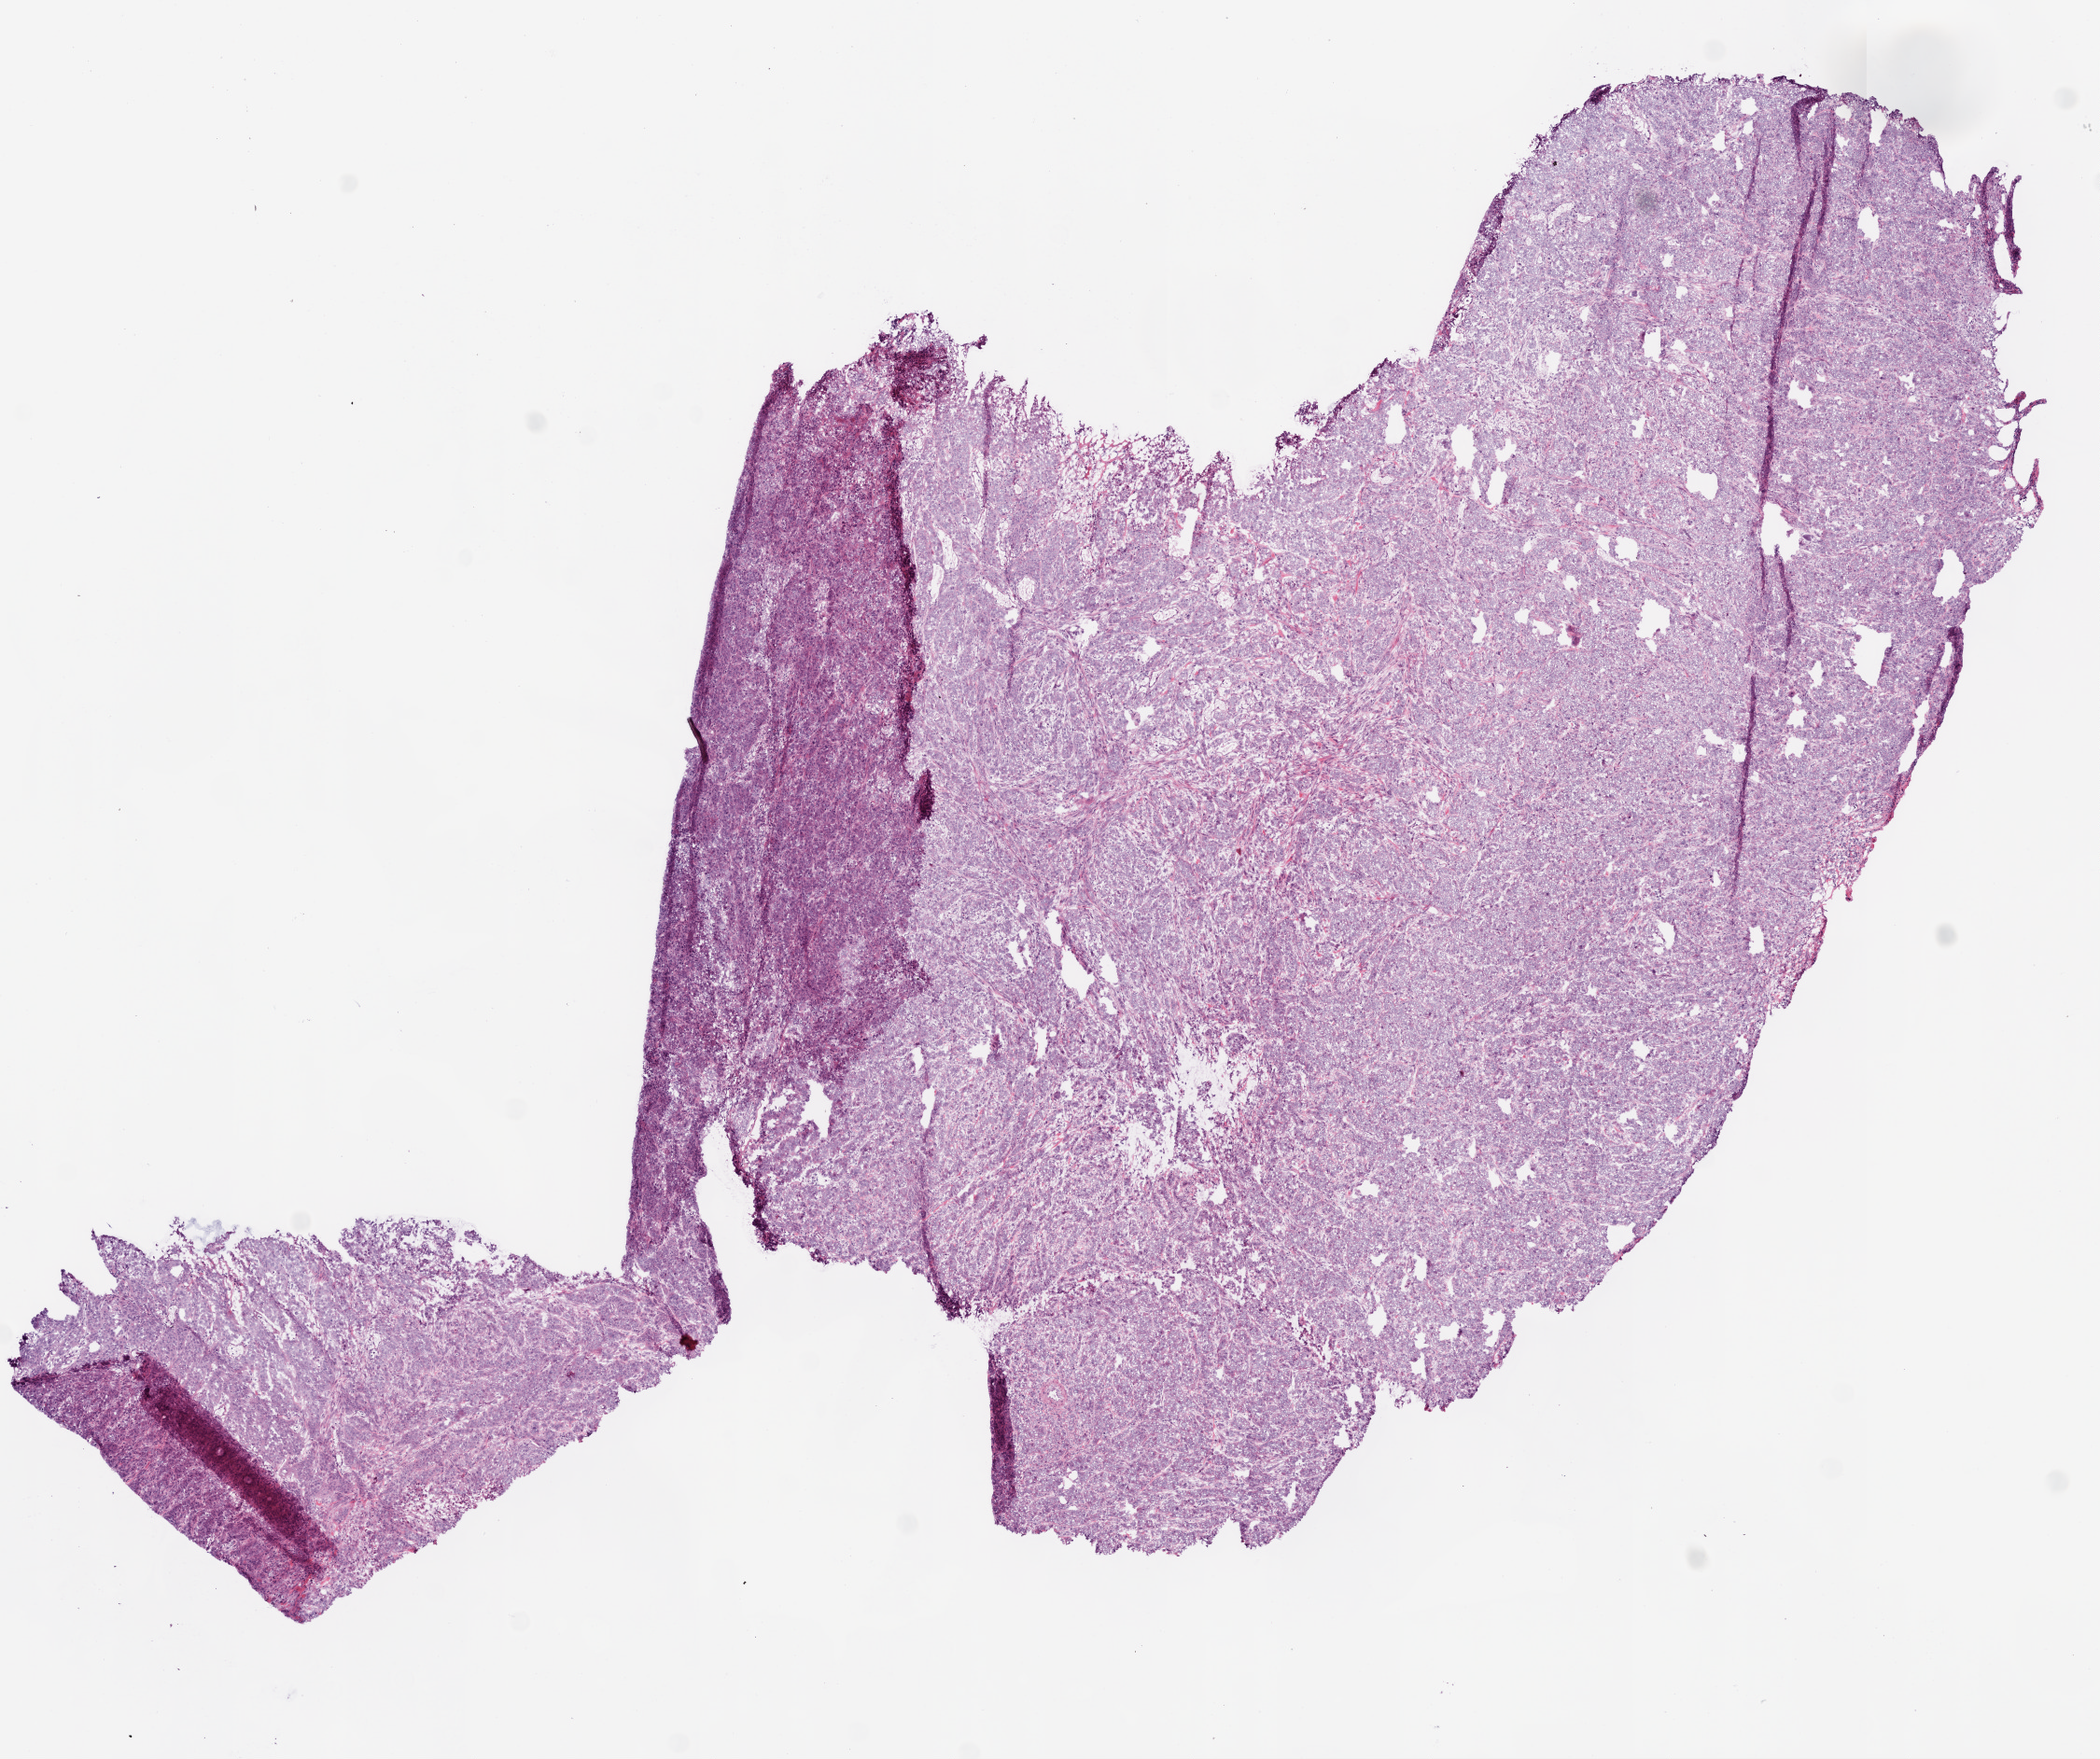
Whole-slide histology image, Hematoxylin and eosin (H&E) stained, low-resolution overview of the scanned area, about 9.0 x 7.6 mm (slide scanned at 20x). Frozen section. Rectum, primary tumour sample. Male, age 51 years at initial diagnosis. Slide review estimates, as recorded: tumour cells 93%, tumour nuclei 90%, normal cells 0%, stromal cells 2%, necrosis 7%.
Lymph nodes positive (case pathology): 0 of 31 examined. AJCC pathologic stage: II (5th edition). TNM: T3 N0 M0. Histologic diagnosis: Adenocarcinoma, NOS.